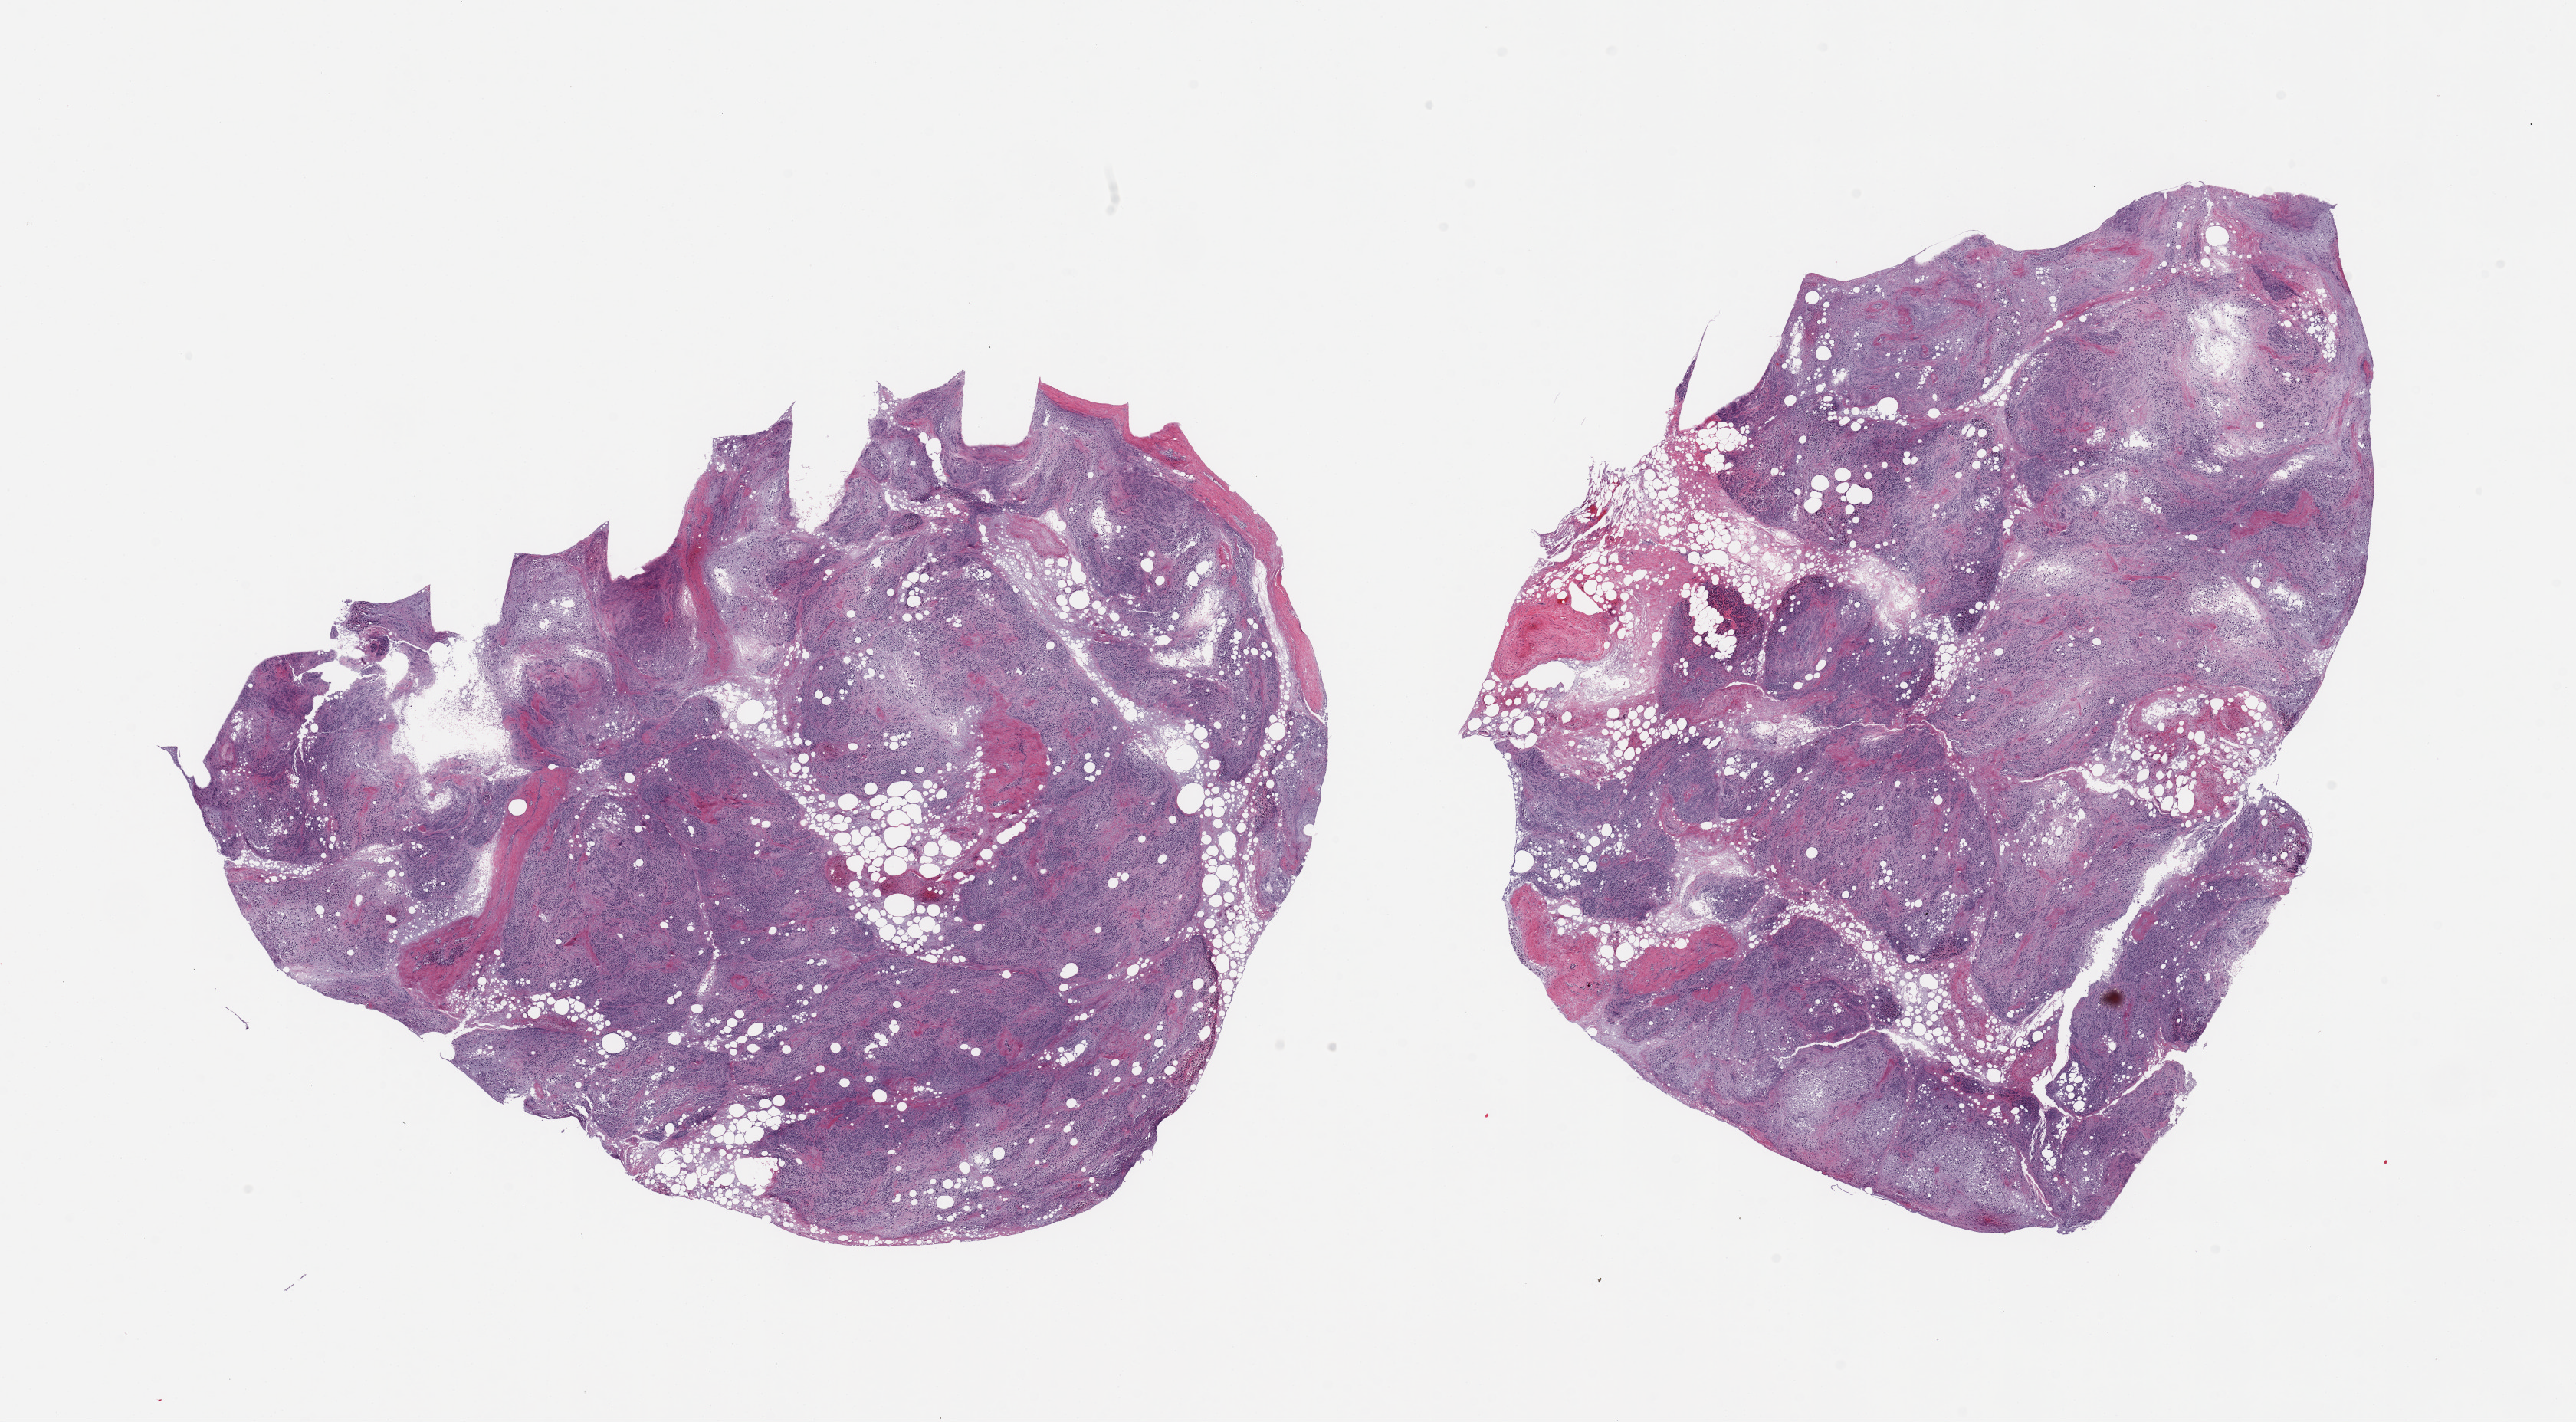
Whole-slide image, hematoxylin and eosin (H&E) stain, a low-resolution overview of the entire scanned area, about 26.6 x 14.7 mm; PAXgene-fixed paraffin-embedded (PFPE) section; section of pancreas (target tissue); tissue donor sample. Donor: male.
Review note (as recorded): 2 pieces, advanced saponification; Islets not visible.